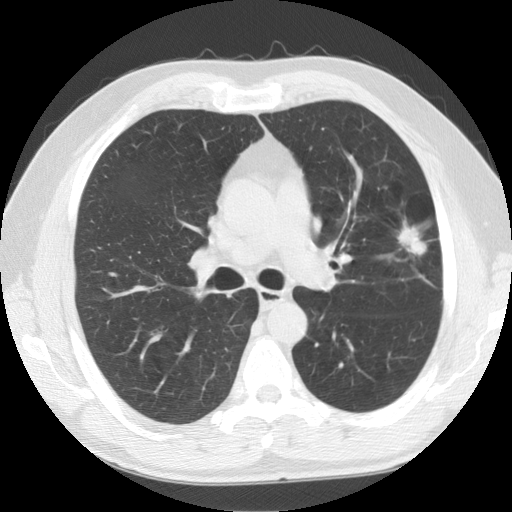
Axial slice from a low-dose chest CT screening exam. First (baseline) screen. Lung window (W 1500 / L -600 HU). Slice 51 of 141 in the series. Male, age 59 years at enrolment. Former smoker at enrolment.
Expert reader's lesion annotation, bounding box (x1, y1, x2, y2) in pixels: (377, 204, 457, 284). Reader record for this screening exam (exam-level; its link to the box is not recorded): non-calcified nodule or mass ≥4 mm, left upper lobe, 23 × 23 mm, spiculated (stellate) margins, soft tissue attenuation. Official screen result: positive, change unspecified: nodule(s) >= 4 mm or enlarging nodule(s), mass(es), or other non-specific abnormalities suspicious for lung cancer. Later outcome: lung cancer diagnosed 28 days after this screen — squamous cell carcinoma, NOS, left upper lobe, moderately differentiated (G2), stage IA (AJCC 6th edition), 27 mm at pathology.